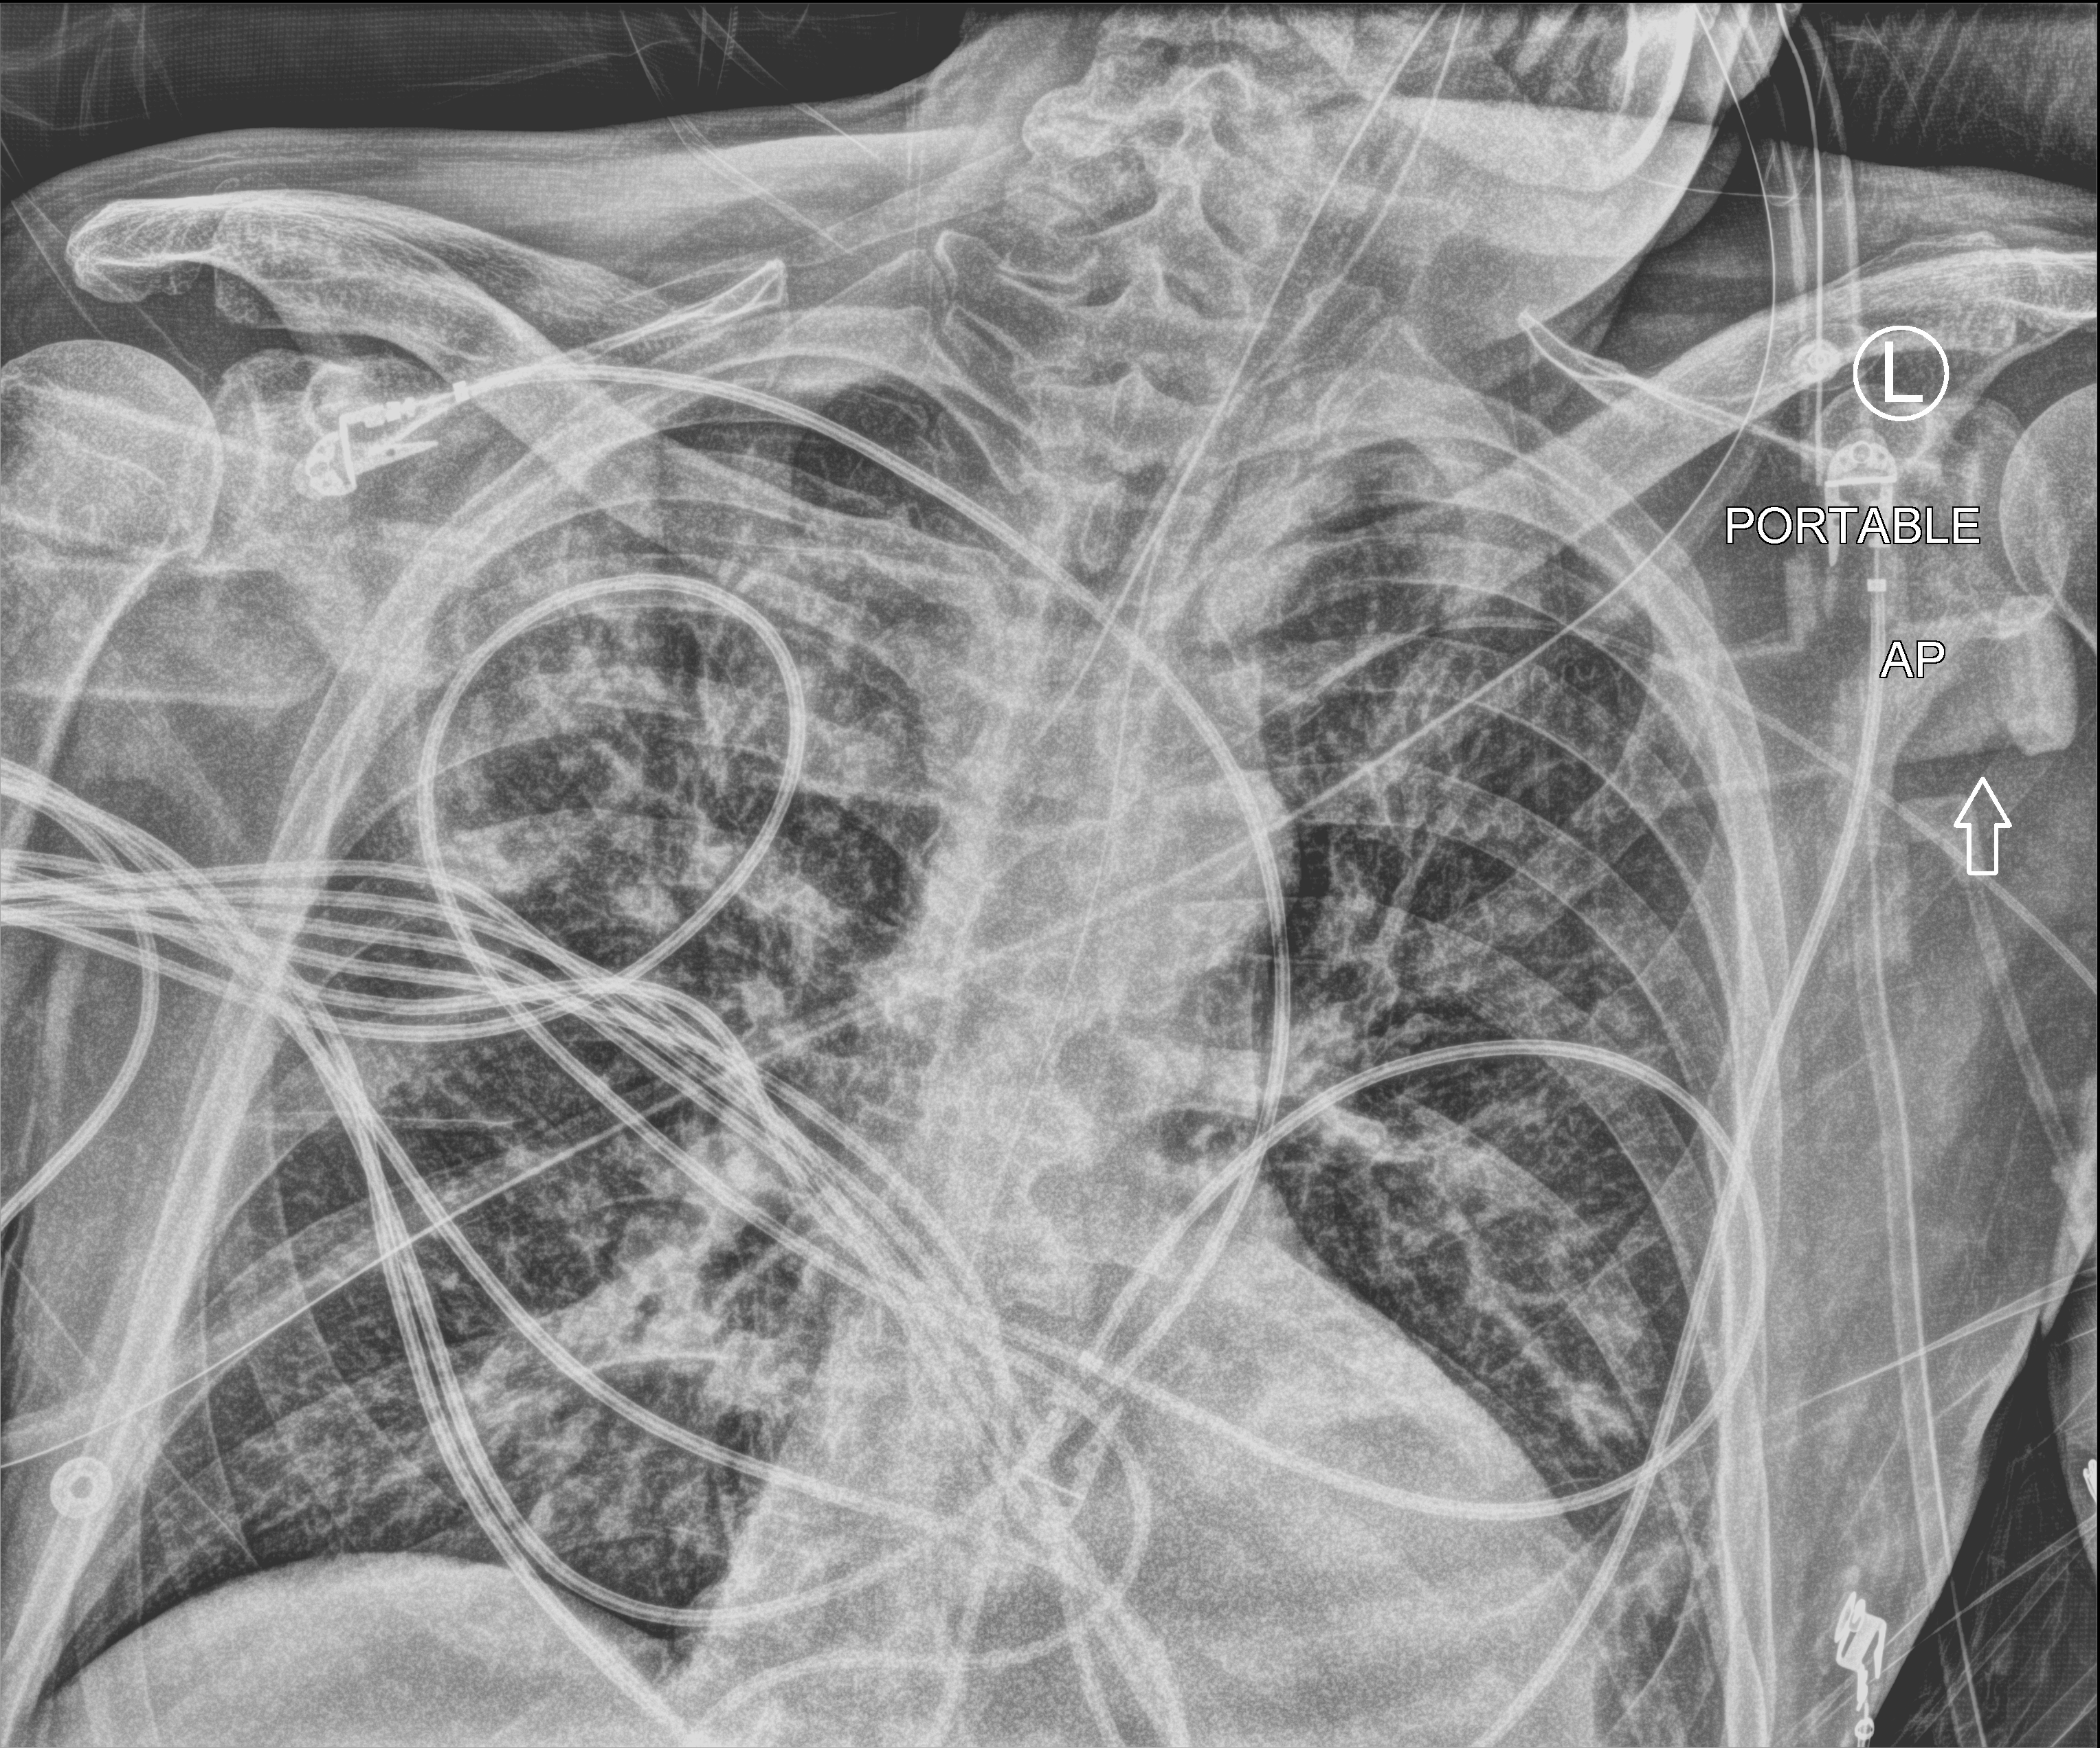
Chest X-ray (portable). Patient hospitalised with COVID-19; male, aged 60–74 years.
Admission-level facts for this patient (not findings on this image; timing relative to this image not recorded):
- hypertension (admission record): yes